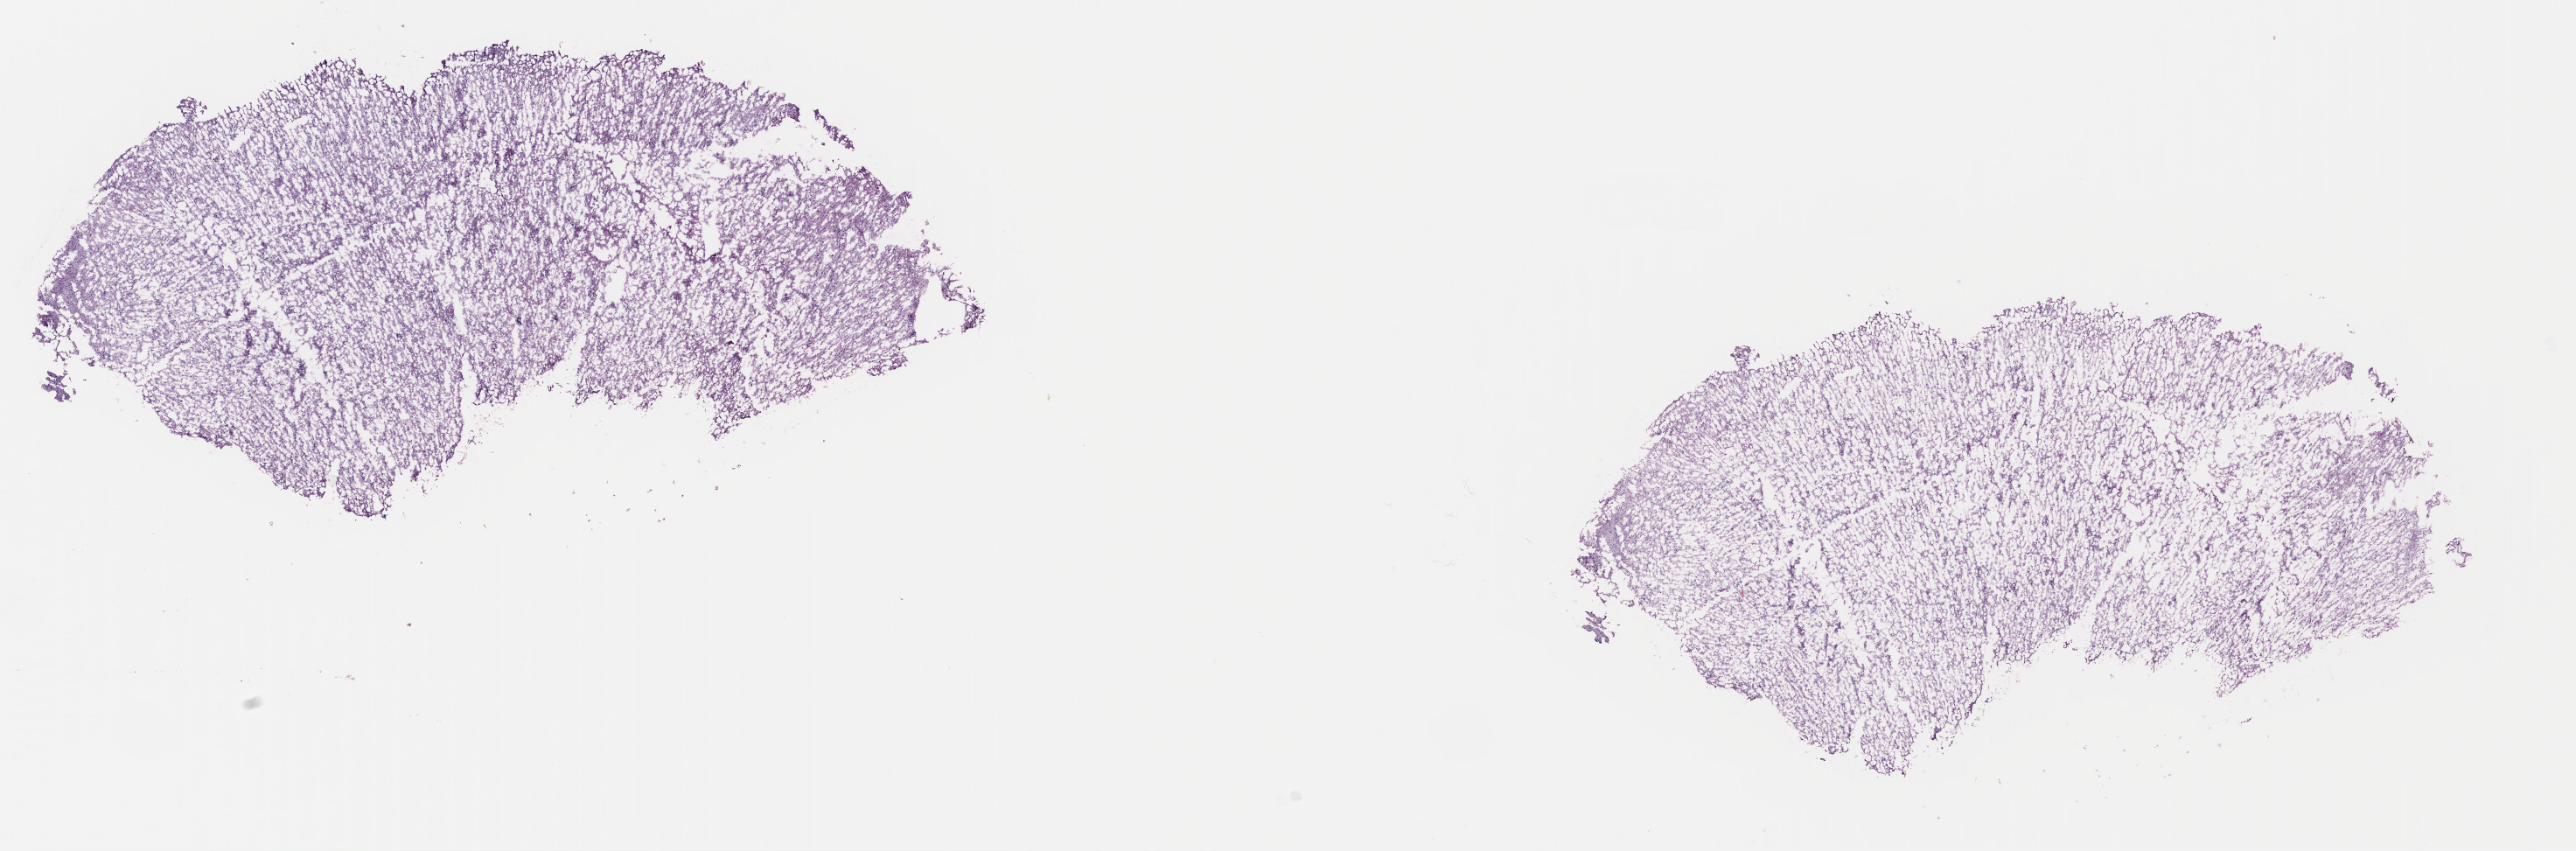
Digitized H&E-stained tissue section (whole slide) — low-resolution overview of the scanned area, about 23.1 x 7.6 mm; frozen section from the top of the tissue portion; sample: primary tumour, brain. Patient: female, age at initial diagnosis 22 years. Histologic grade: G2 (moderately differentiated). Composition of this section per pathologist review: tumour cells 45%, tumour nuclei 80%, normal cells 10%, stromal cells 45%, necrosis 0%. Infiltration values recorded for this section: lymphocyte infiltration 0%, monocyte infiltration 0%, neutrophil infiltration 0%.
Pathologic diagnosis: Mixed glioma (cerebrum).